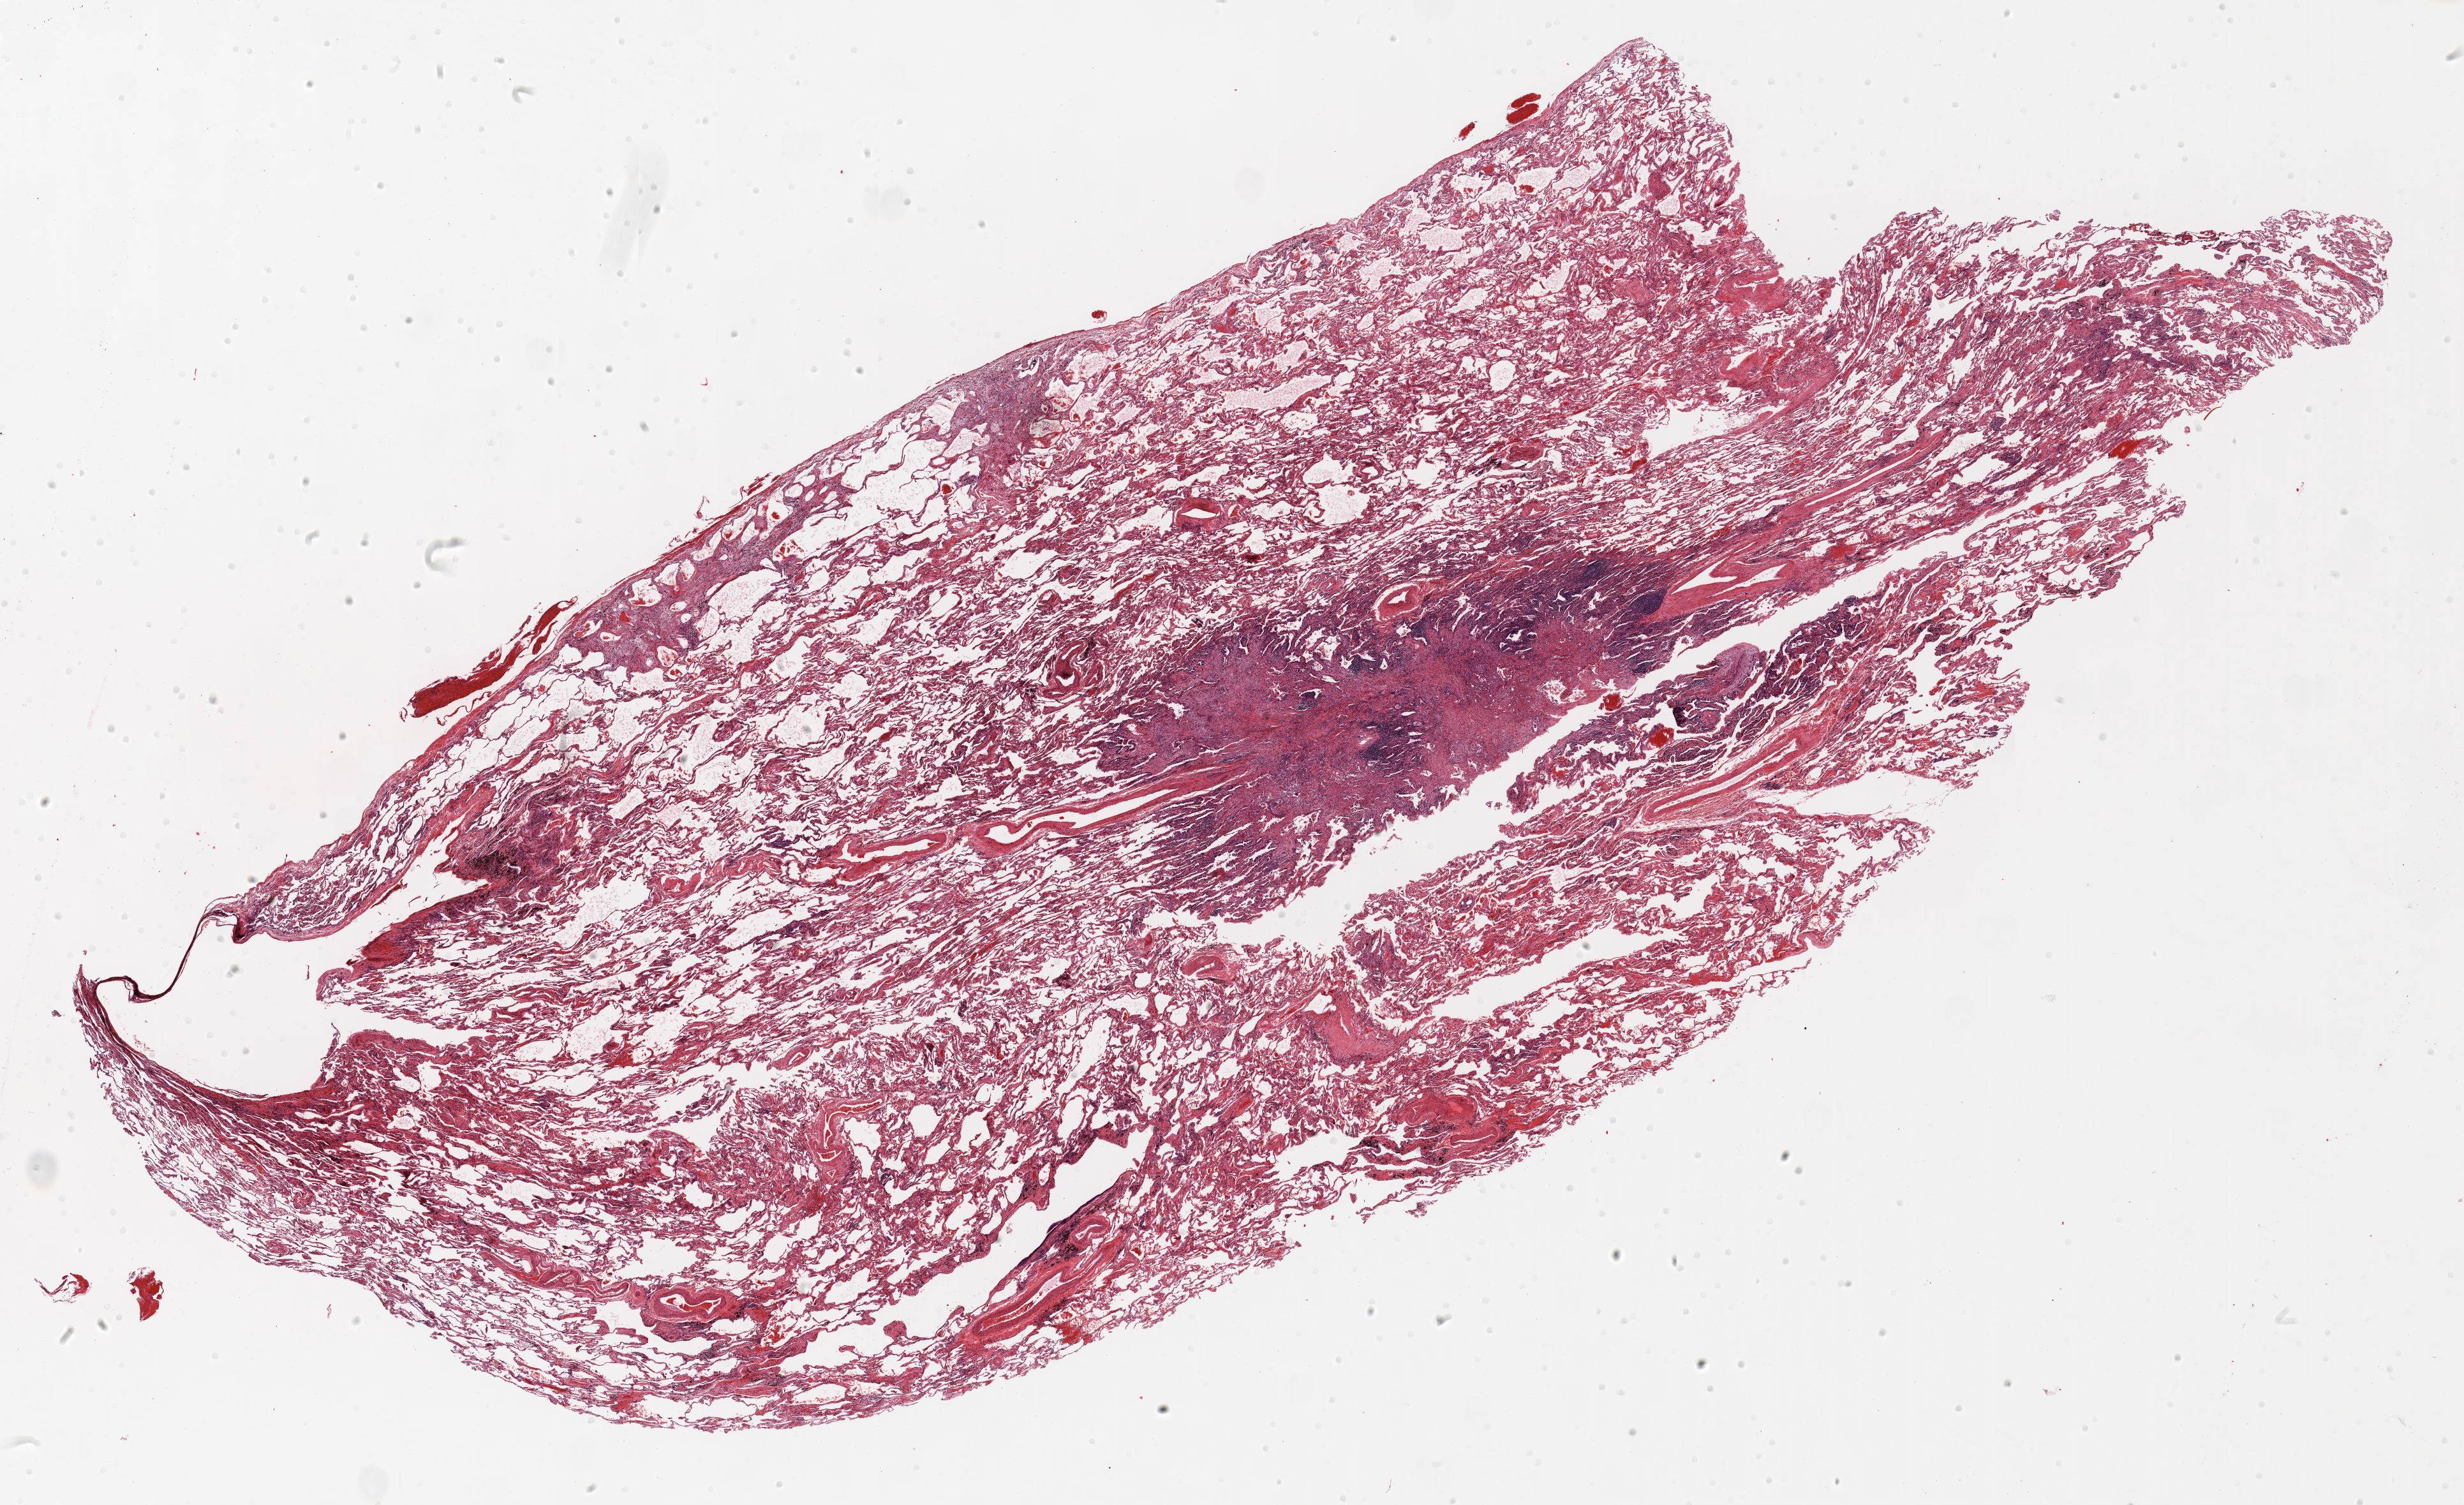
H&E-stained whole-slide image — a low-resolution overview of the entire scanned area, about 31.0 x 19.0 mm (acquisition: 20x scan), FFPE section, lung. Female, age 72 at enrolment. Former smoker at enrolment. Grade: well differentiated (G1).
Primary tumour location (clinical record): right upper lobe. Stage (AJCC 6th edition): IA. Participant's lung-cancer diagnosis: Bronchiolo-alveolar adenocarcinoma, NOS (ICD-O-3 8250/3). Tumour size (pathology): 8 mm.